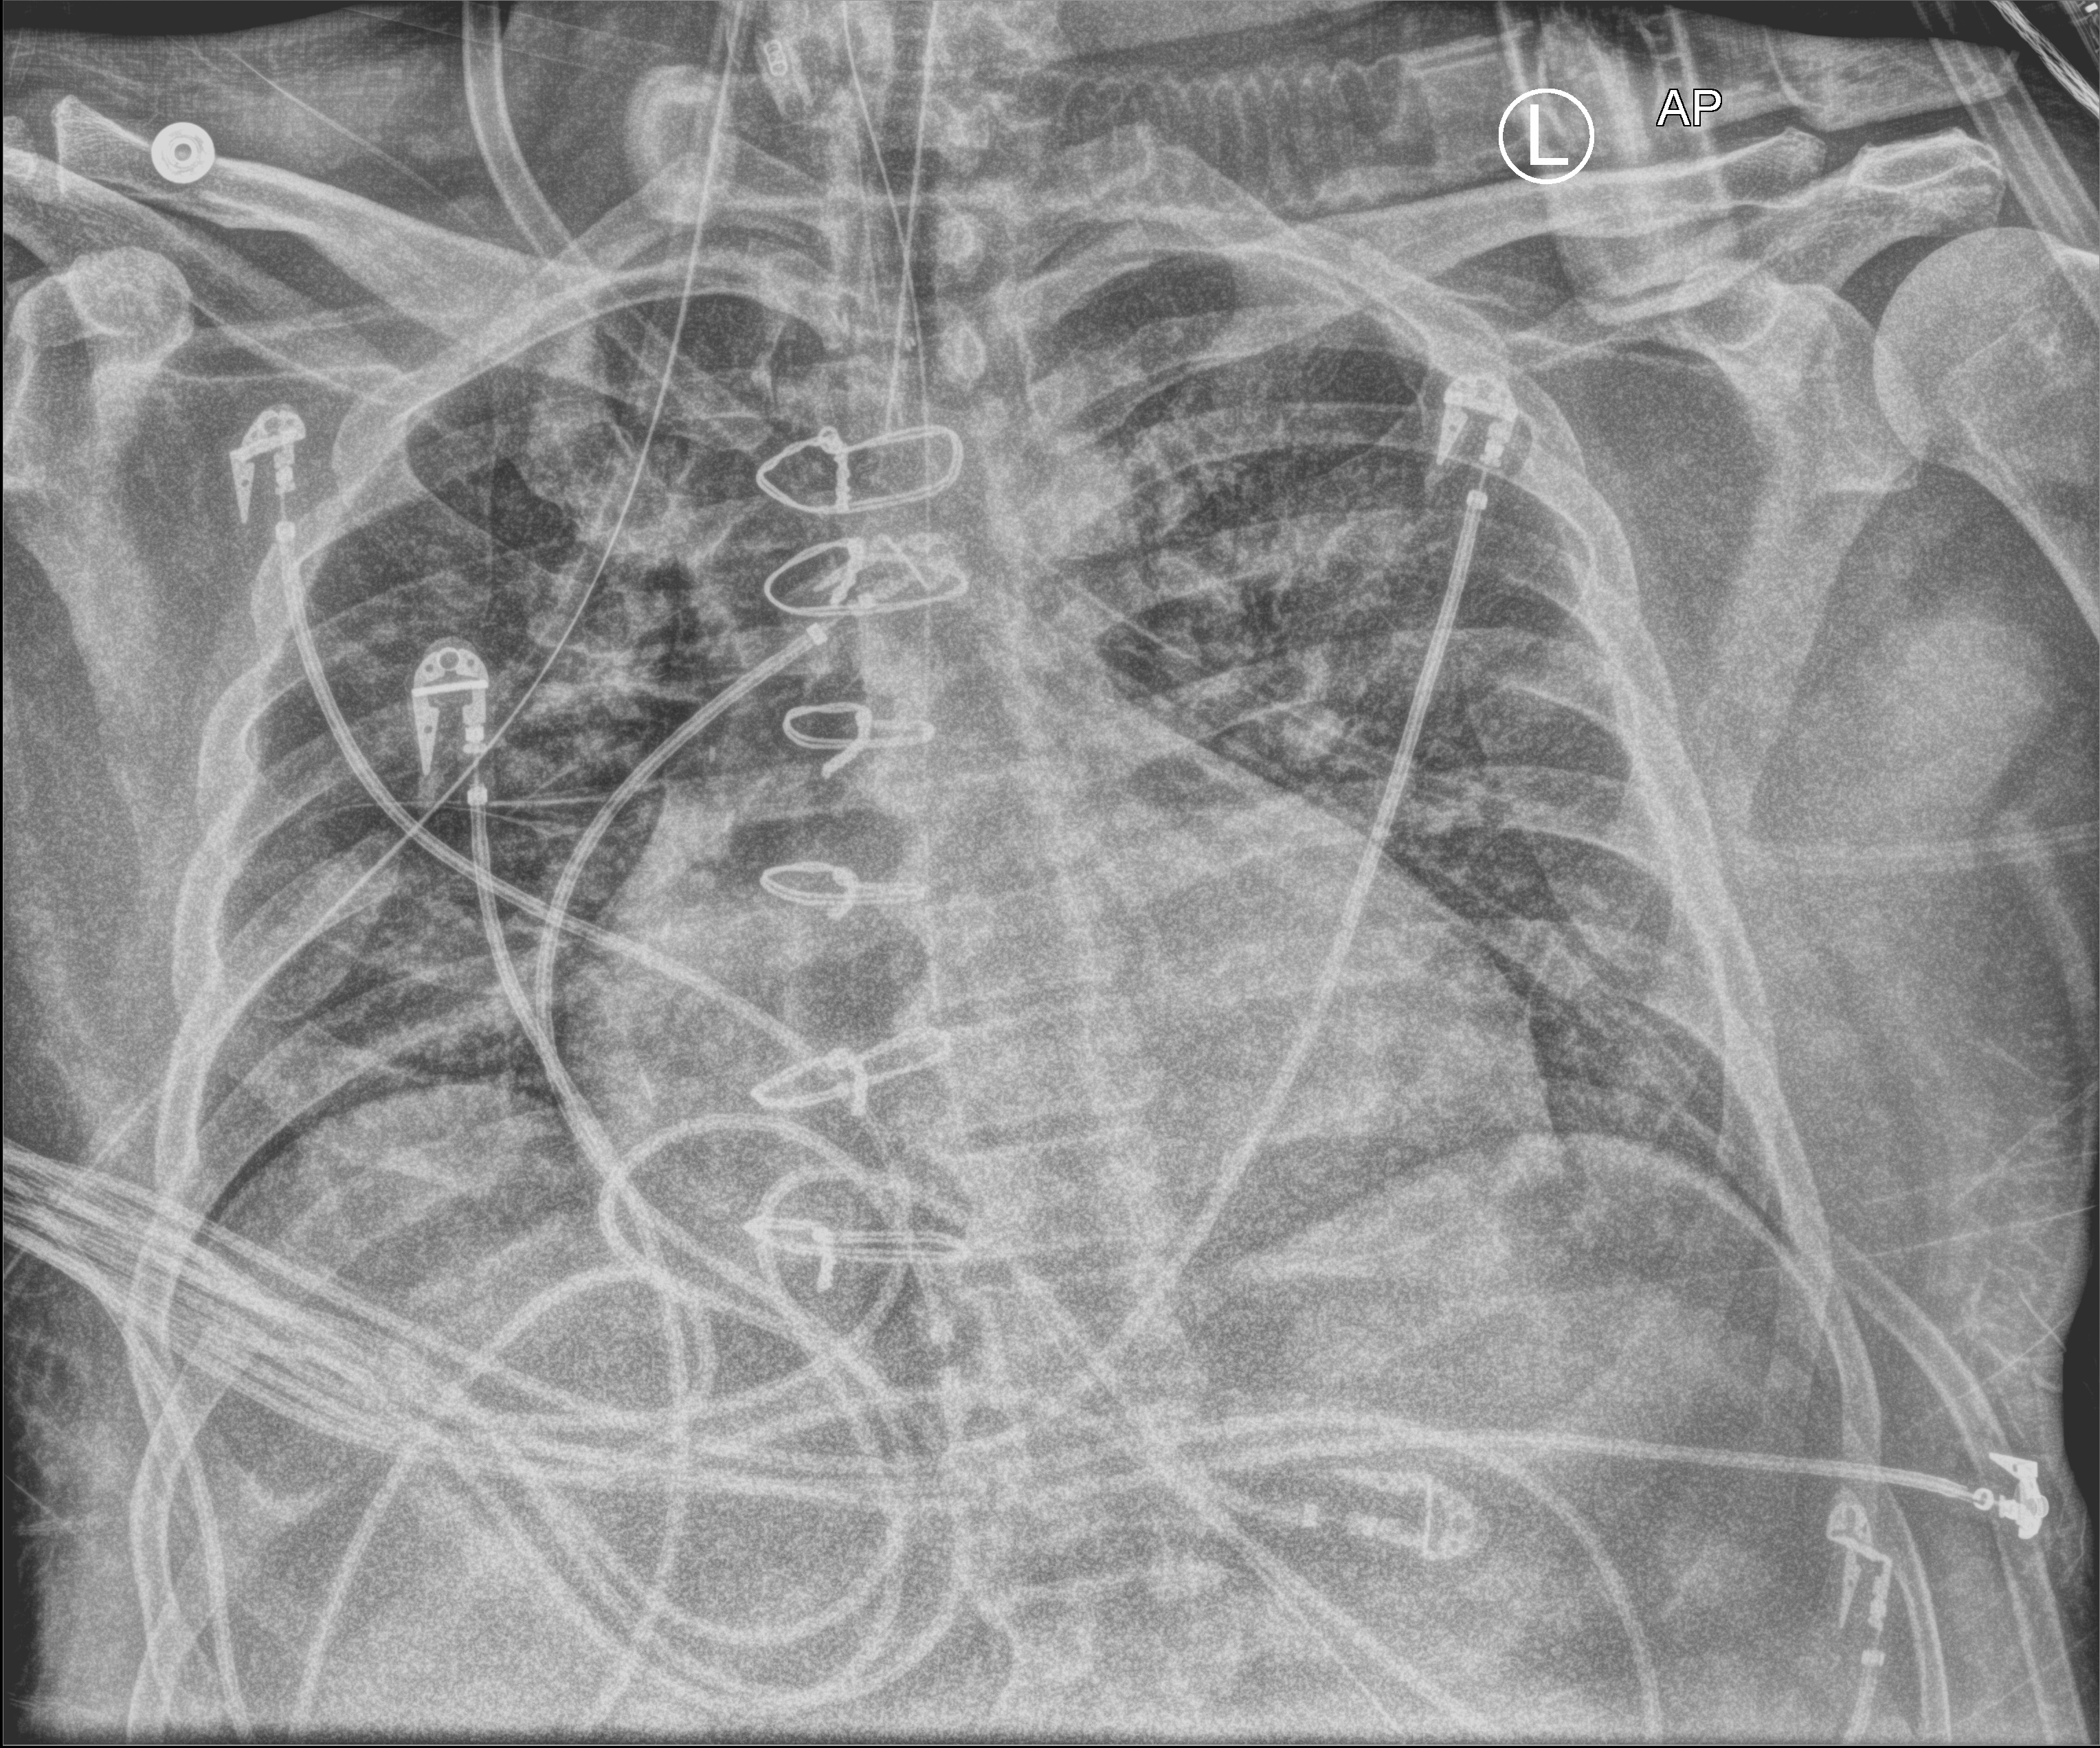
Portable chest radiograph, anteroposterior (AP) projection. Adult patient hospitalised with COVID-19, age 18–59 years.
From the hospital-stay record, not from the radiograph (when in the stay this image was taken is not recorded): admitted to intensive care during this hospital stay: yes.